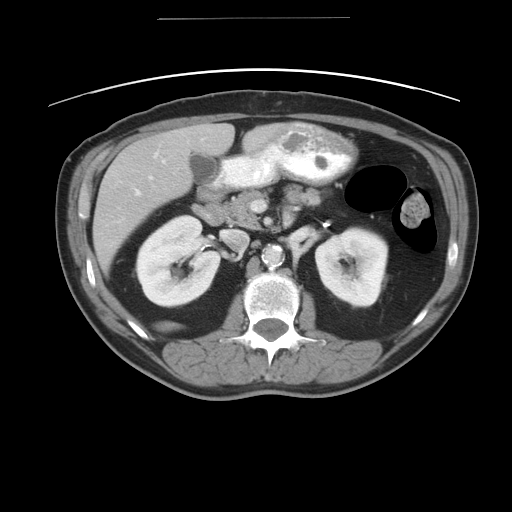
Contrast-enhanced abdominal CT, one axial slice. Slice 21 of 49 in the series (ordered by position). Intravenous contrast given. Soft-tissue window (W 400 / L 40 HU). 5 mm slice thickness. 512 × 512 image matrix, field of view 413 × 413 mm. Male patient, age 57 years. From the clinical record (not read from this slice): diagnosis: colorectal cancer liver metastases, imaged before liver resection; multiple liver metastases: yes; largest metastasis: 4 cm; disease in both lobes: no.
Outlined on this slice (manually delineated by an expert):
- hepatic veins: bounding box <148,151,158,178> (left, top, right, bottom; pixels)
- liver: <93,123,283,273>
- planned liver remnant (the part of the liver to remain after resection): <214,123,284,152>
- portal vein (with intrahepatic branches): <135,158,165,194>